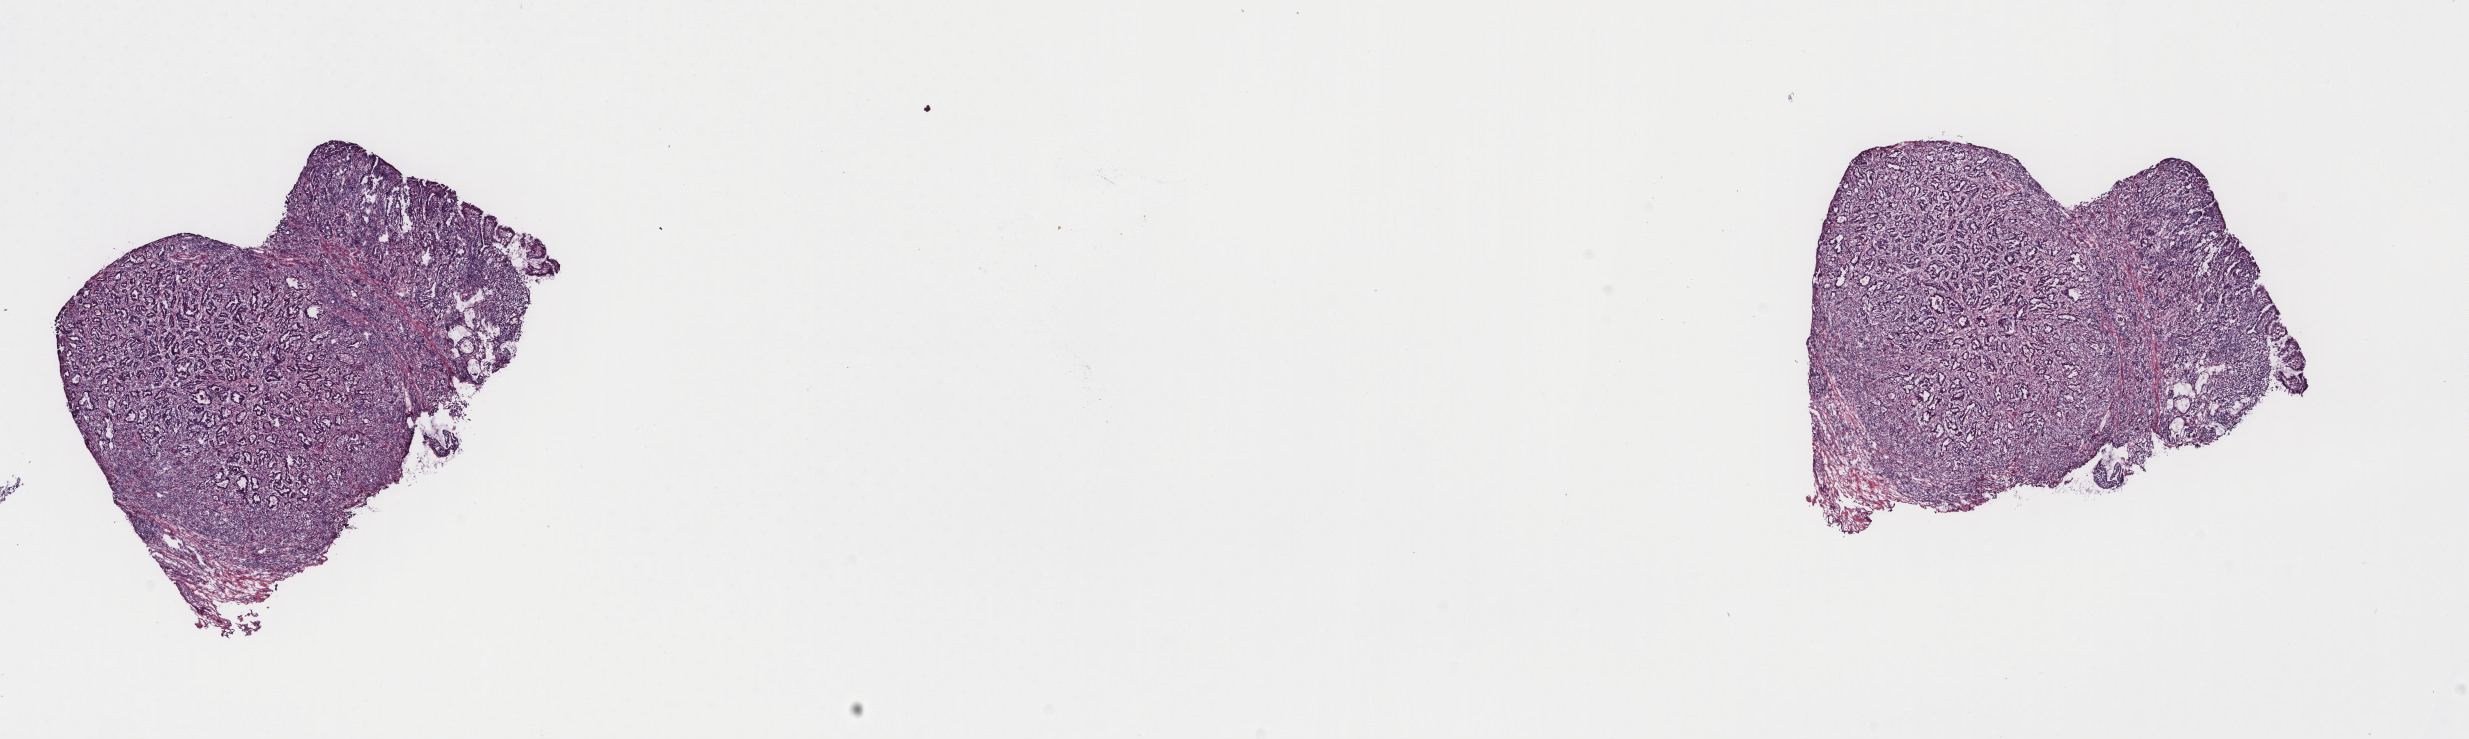
Digitized H&E tissue section (whole slide) — low-resolution overview of the scanned area, about 19.6 x 5.9 mm (acquisition: 40x scan), frozen section, stomach, primary tumour sample. Male patient; age at initial diagnosis 61 years. Histologic grade: G2 (moderately differentiated). Slide review estimates, as recorded: tumour cells 100%, tumour nuclei 65%, normal cells 0%, stromal cells 0%, necrosis 0%. Inflammatory infiltration, as recorded: lymphocyte infiltration 15%, monocyte infiltration 1%, neutrophil infiltration 1%.
AJCC pathologic stage: IIA. Histologic diagnosis: Tubular adenocarcinoma (gastric antrum). Lymph nodes positive (case pathology): 1 of 47 examined.